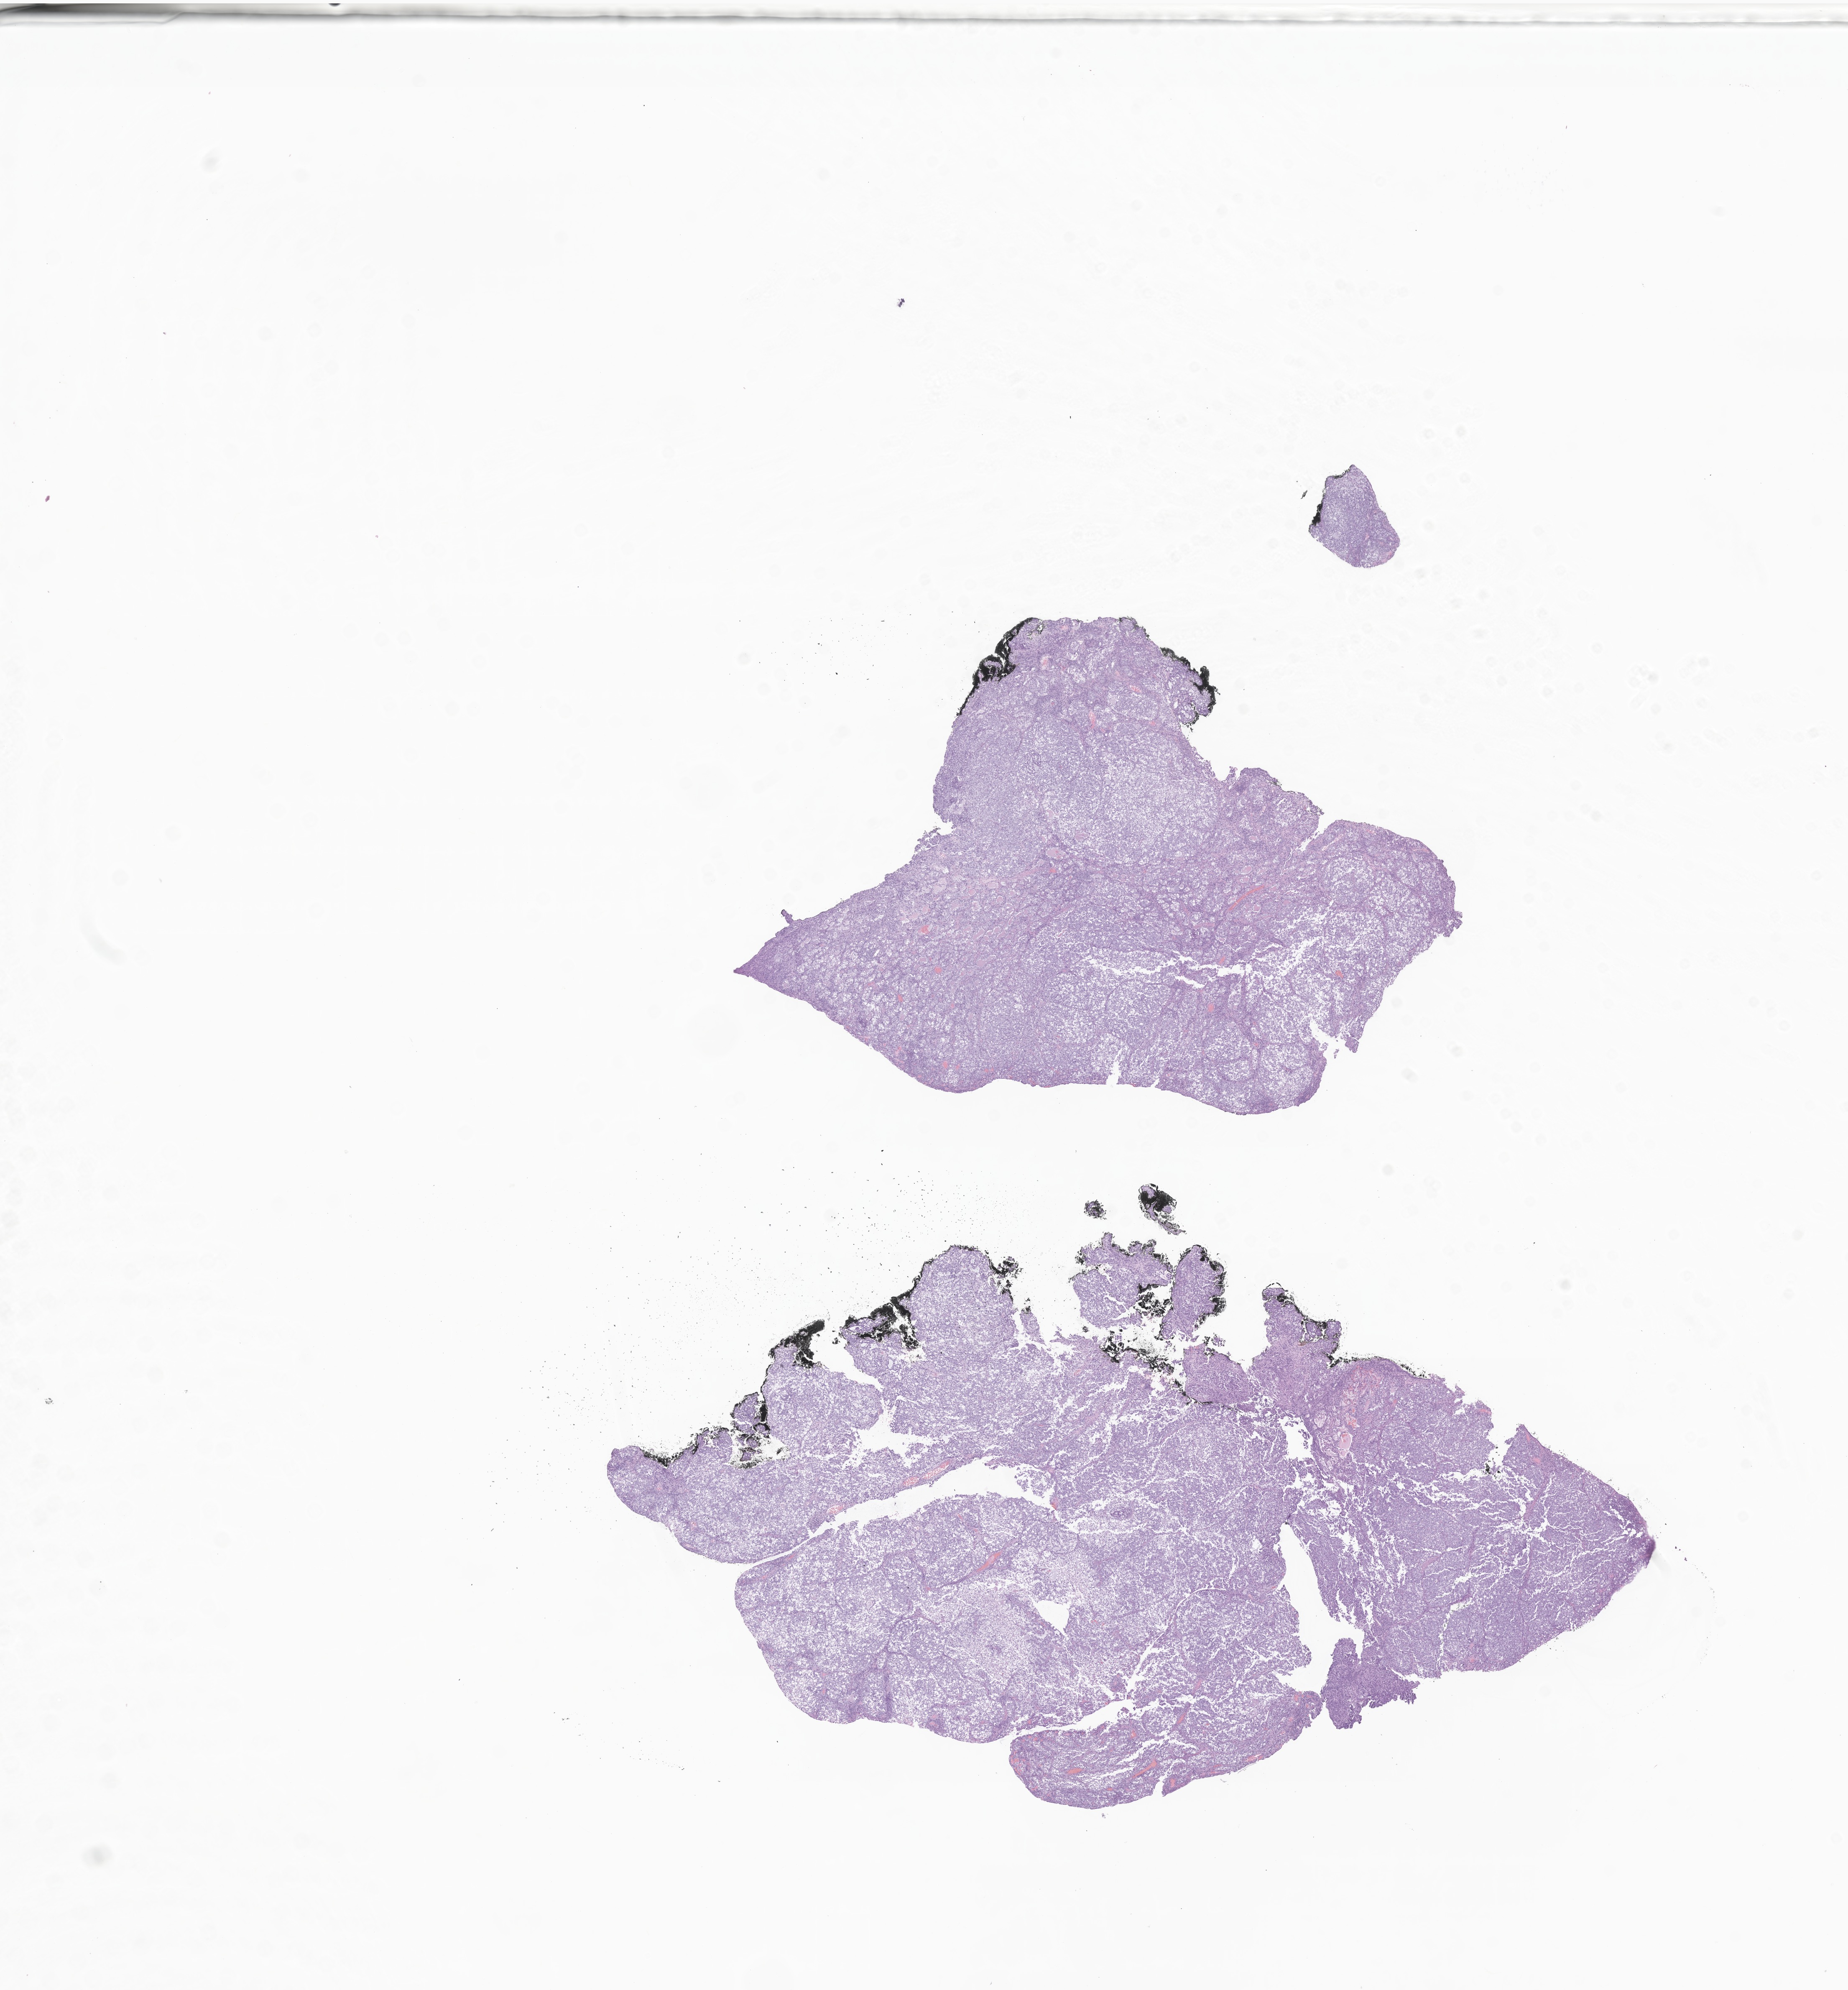
Digitized hematoxylin and eosin (H&E)-stained section of tumor tissue from the vagina, a low-resolution overview of the entire scanned area, about 18.6 x 20.1 mm, FFPE section. Female patient, age 213 months (17 years 9 months).
Recorded diagnosis: Clear cell adenocarcinoma, NOS.